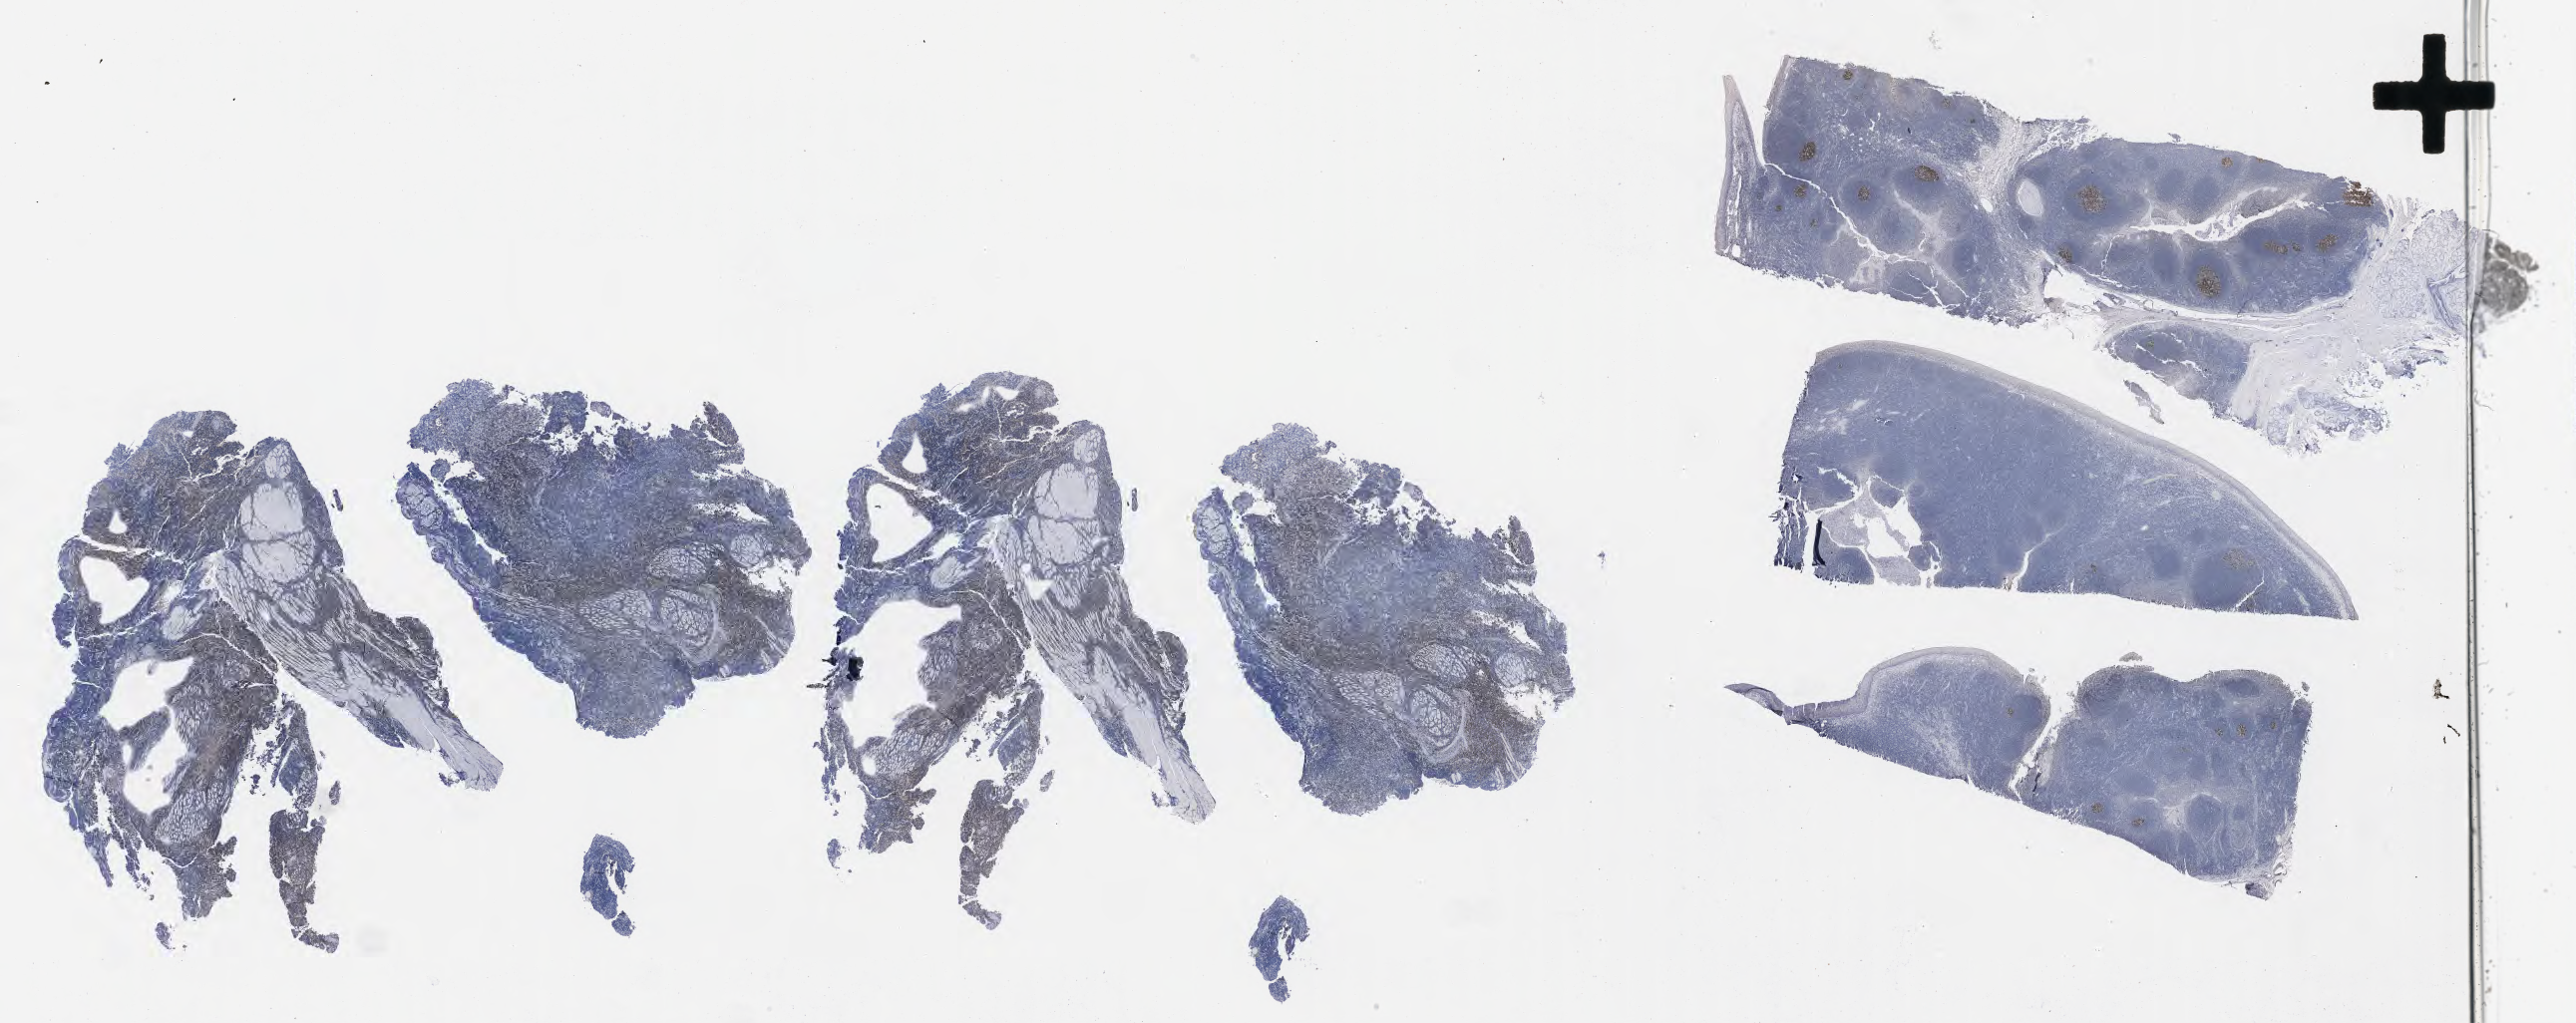
Whole-slide image, immunohistochemical stain for BCL6, low-resolution overview of the scanned area, about 41.7 x 16.6 mm, tumor tissue, site: pelvis. Male patient; age at initial diagnosis 7 years.
Histologic diagnosis: Diffuse large B-cell lymphoma, NOS.